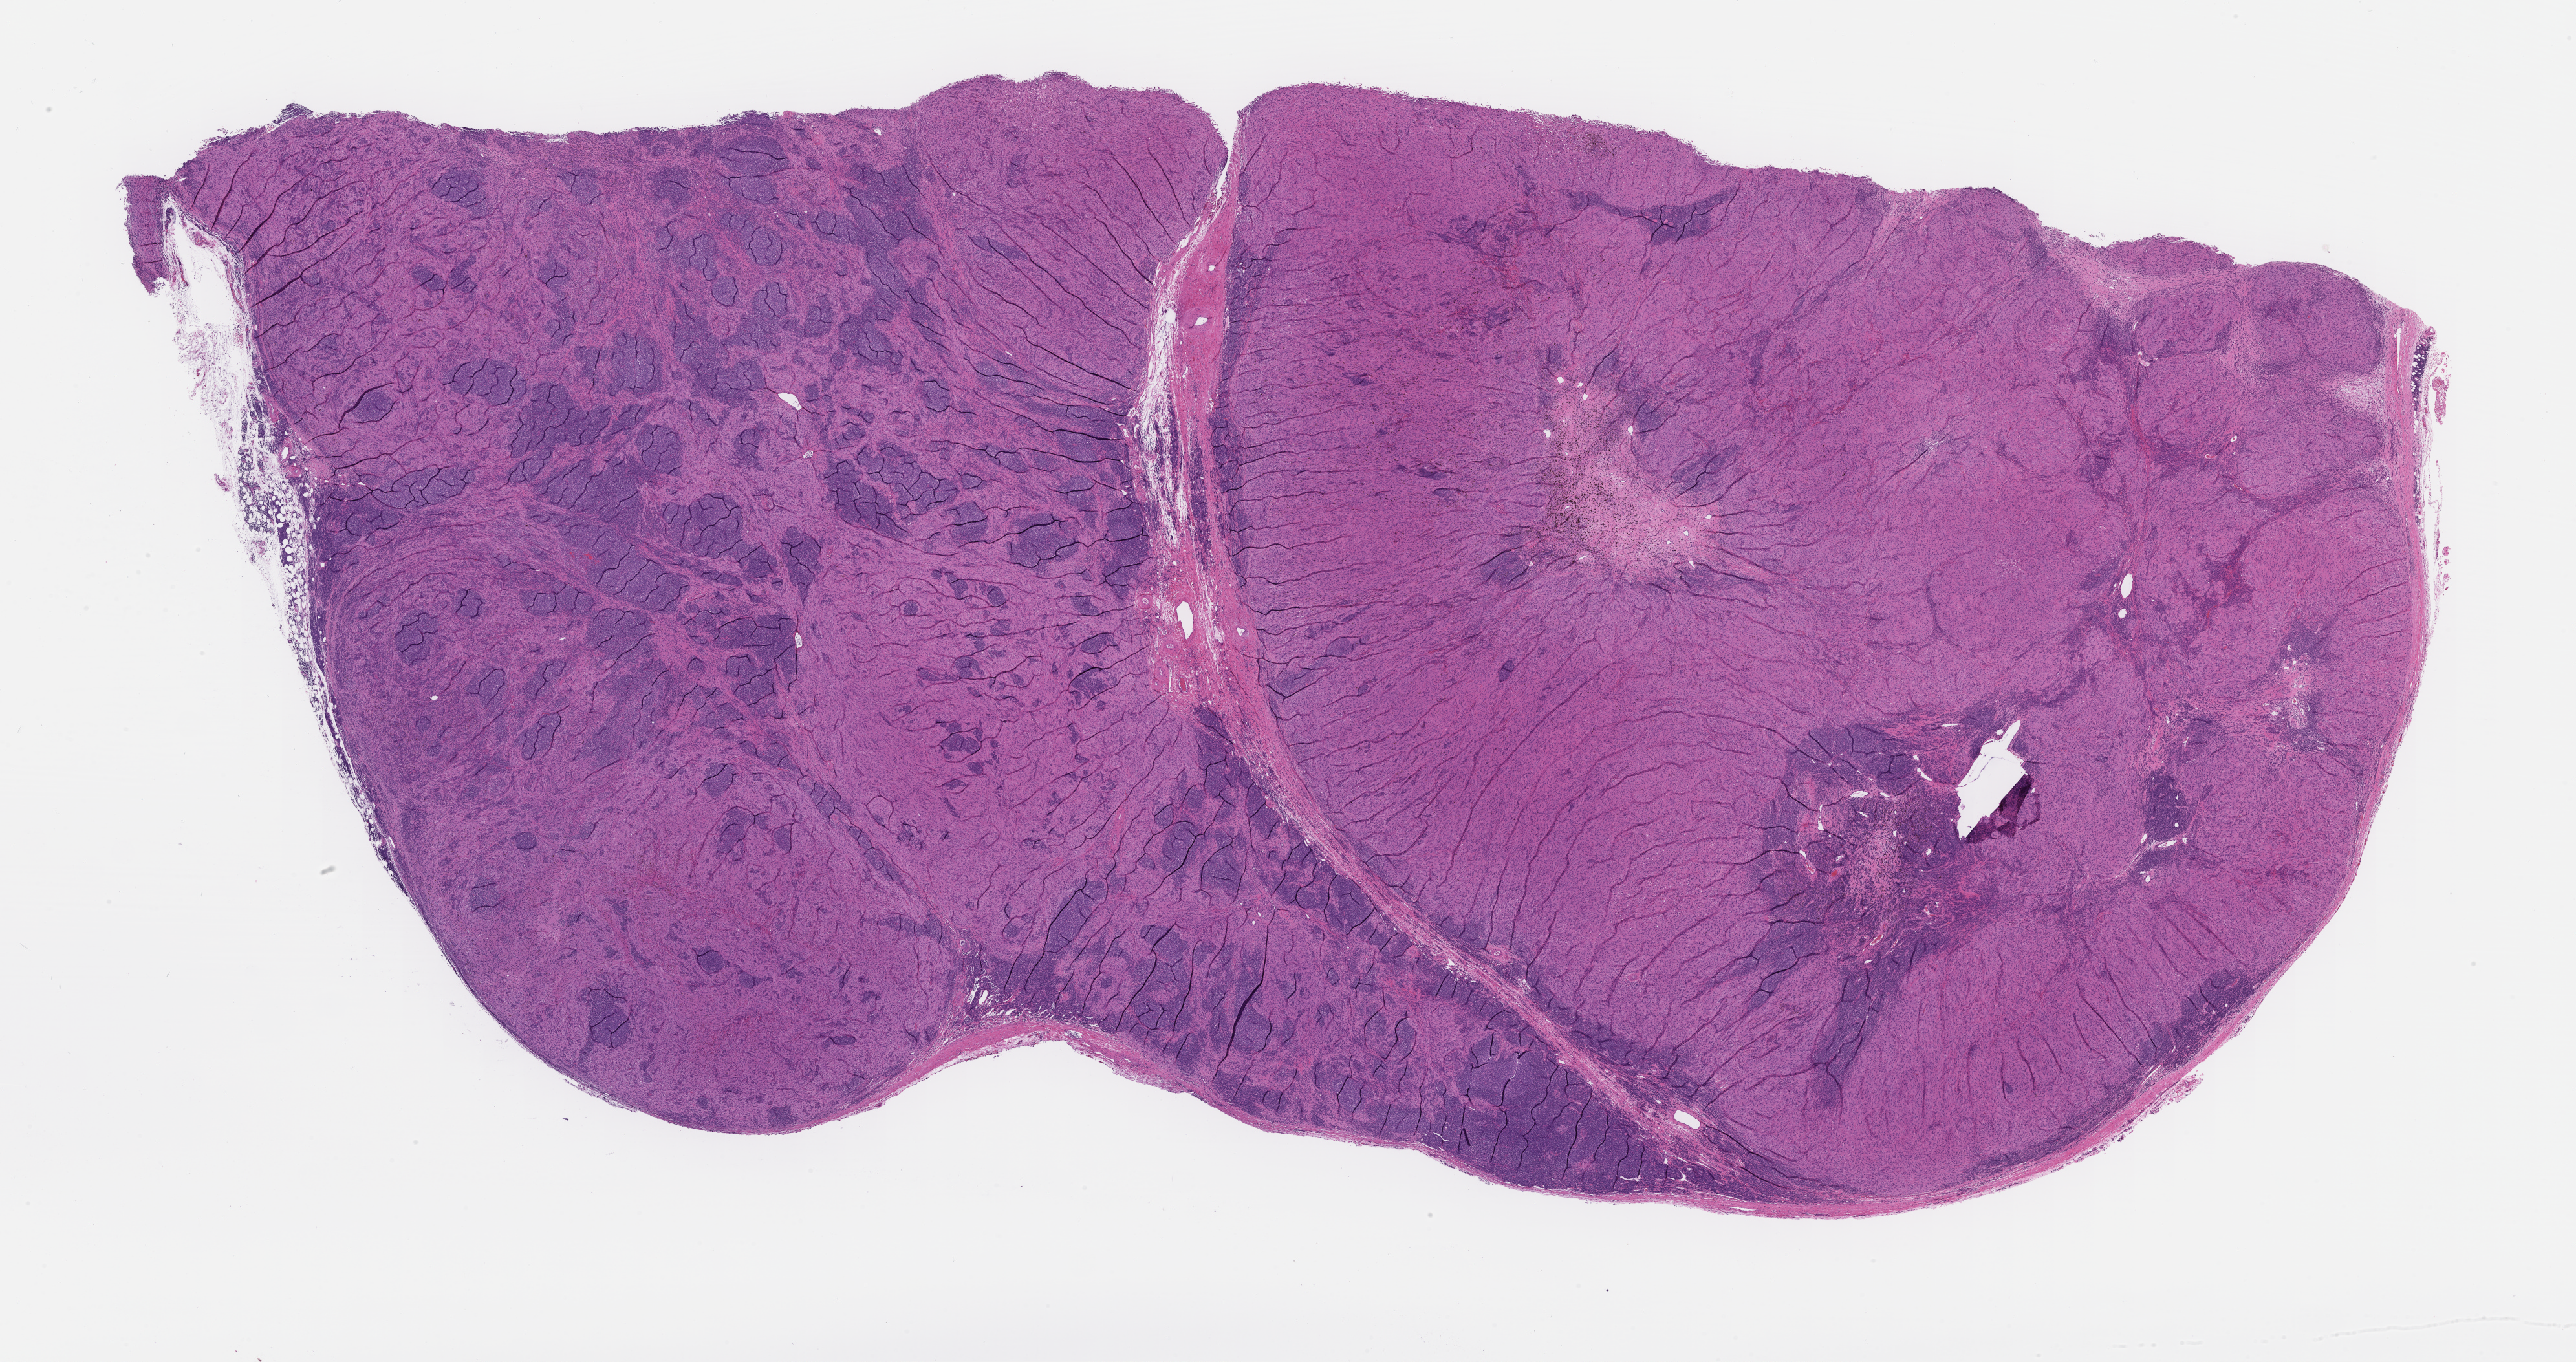
Digitized hematoxylin and eosin (H&E)-stained section — whole scanned area (about 32.2 x 17.0 mm) shown as a low-resolution overview; formalin-fixed paraffin-embedded section; specimen time point: collected at baseline (before treatment). Patient sex: female.
This section: metastasis (sampled organ not recorded). Patient diagnosis (primary): Melanoma.